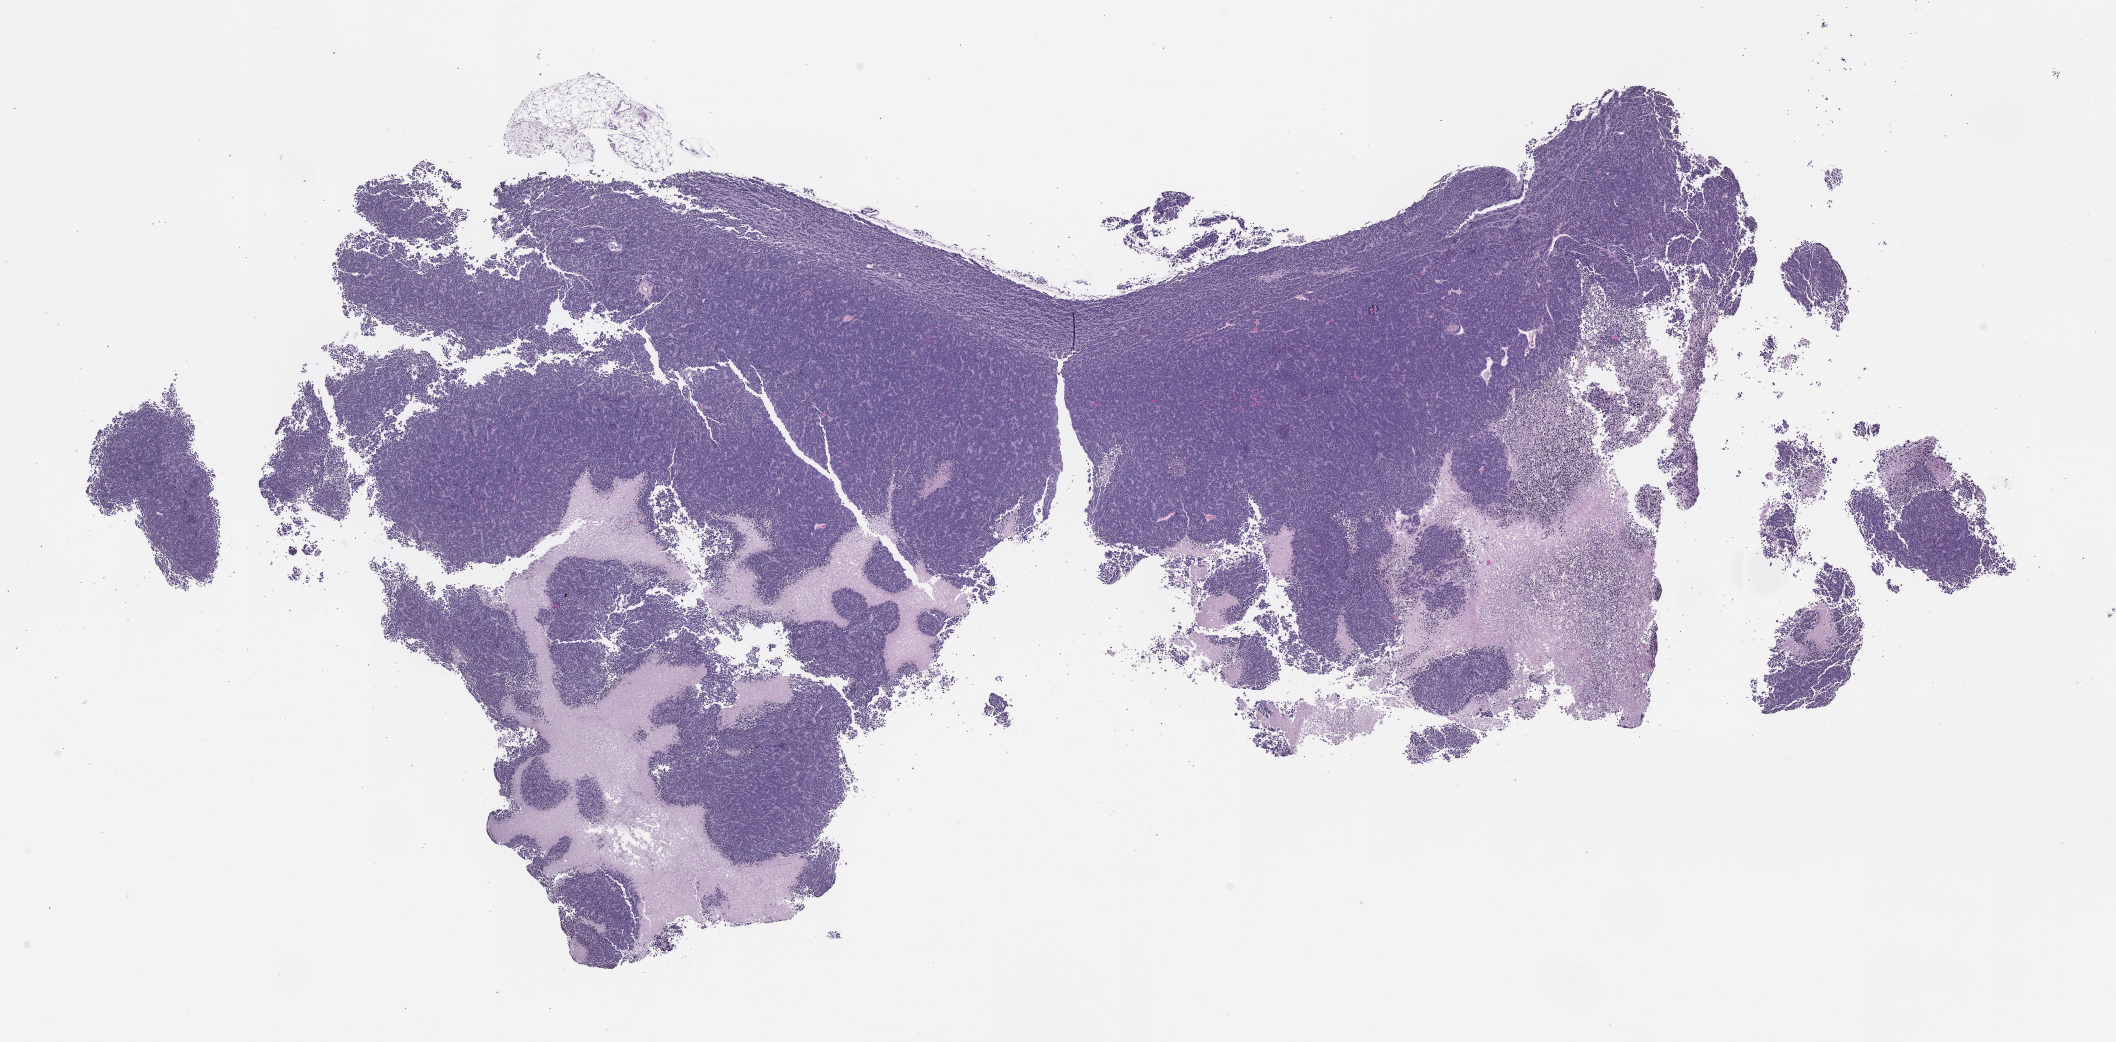
Hematoxylin and eosin (H&E) whole-slide image of a patient-derived xenograft (PDX) tumor grown in a mouse, passage 3, a low-resolution overview of the entire scanned area, about 17.0 x 8.4 mm, FFPE section, originating tumor site category: musculoskeletal.
* originating patient diagnosis: Ewing Sarcoma|Primitive Neuroectodermal Tumor